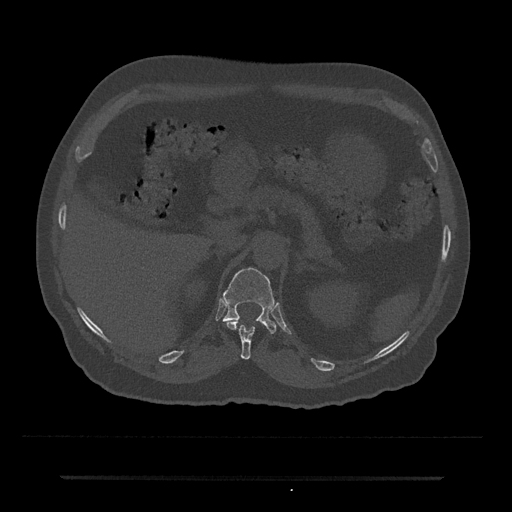
CT including the spine, one axial slice; position 147 of 797 along the scan axis; reconstruction kernel Br40s/3; 120 kVp; bone window (W 1800 / L 400 HU); 0.5 mm slice thickness; 512 × 512 image matrix. Male patient, age 69 years. Case-level facts recorded for this patient, not image findings: primary cancer: prostate.
Annotated regions visible in this slice (semi-automatically segmented with operator editing):
- T11 vertebra: bounding box (x1, y1, x2, y2) in pixels: (226, 321, 255, 360)
- T12 vertebra: (218, 267, 276, 333)